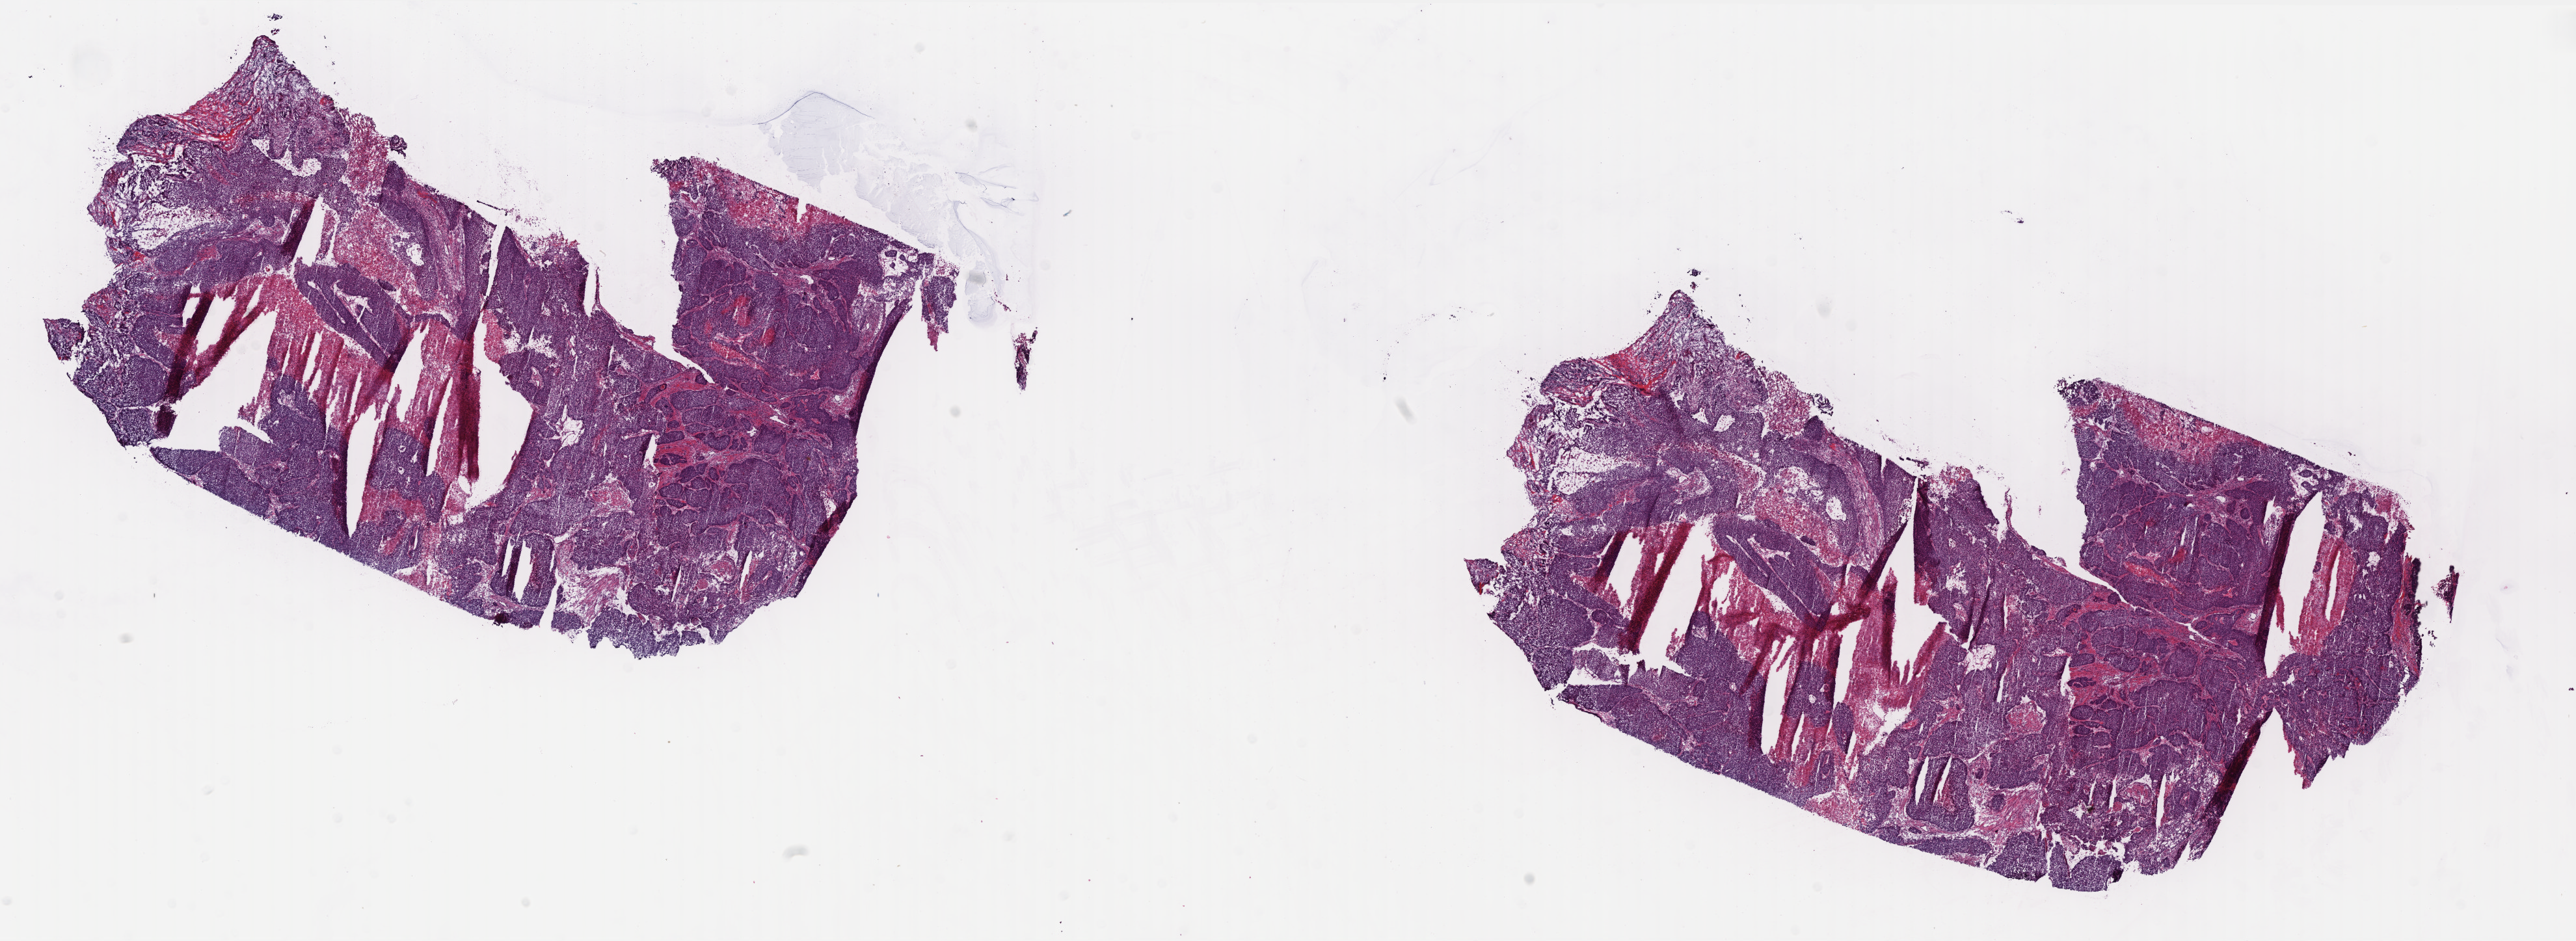
Hematoxylin and eosin (H&E) stained whole-slide image, a low-resolution overview of the entire scanned area, about 31.7 x 11.6 mm (from a 40x scan). Frozen section from the bottom of the tissue portion. Primary tumour sample from the breast. Patient: female, age at initial diagnosis 57 years.
Pathologic diagnosis: Infiltrating duct carcinoma, NOS.